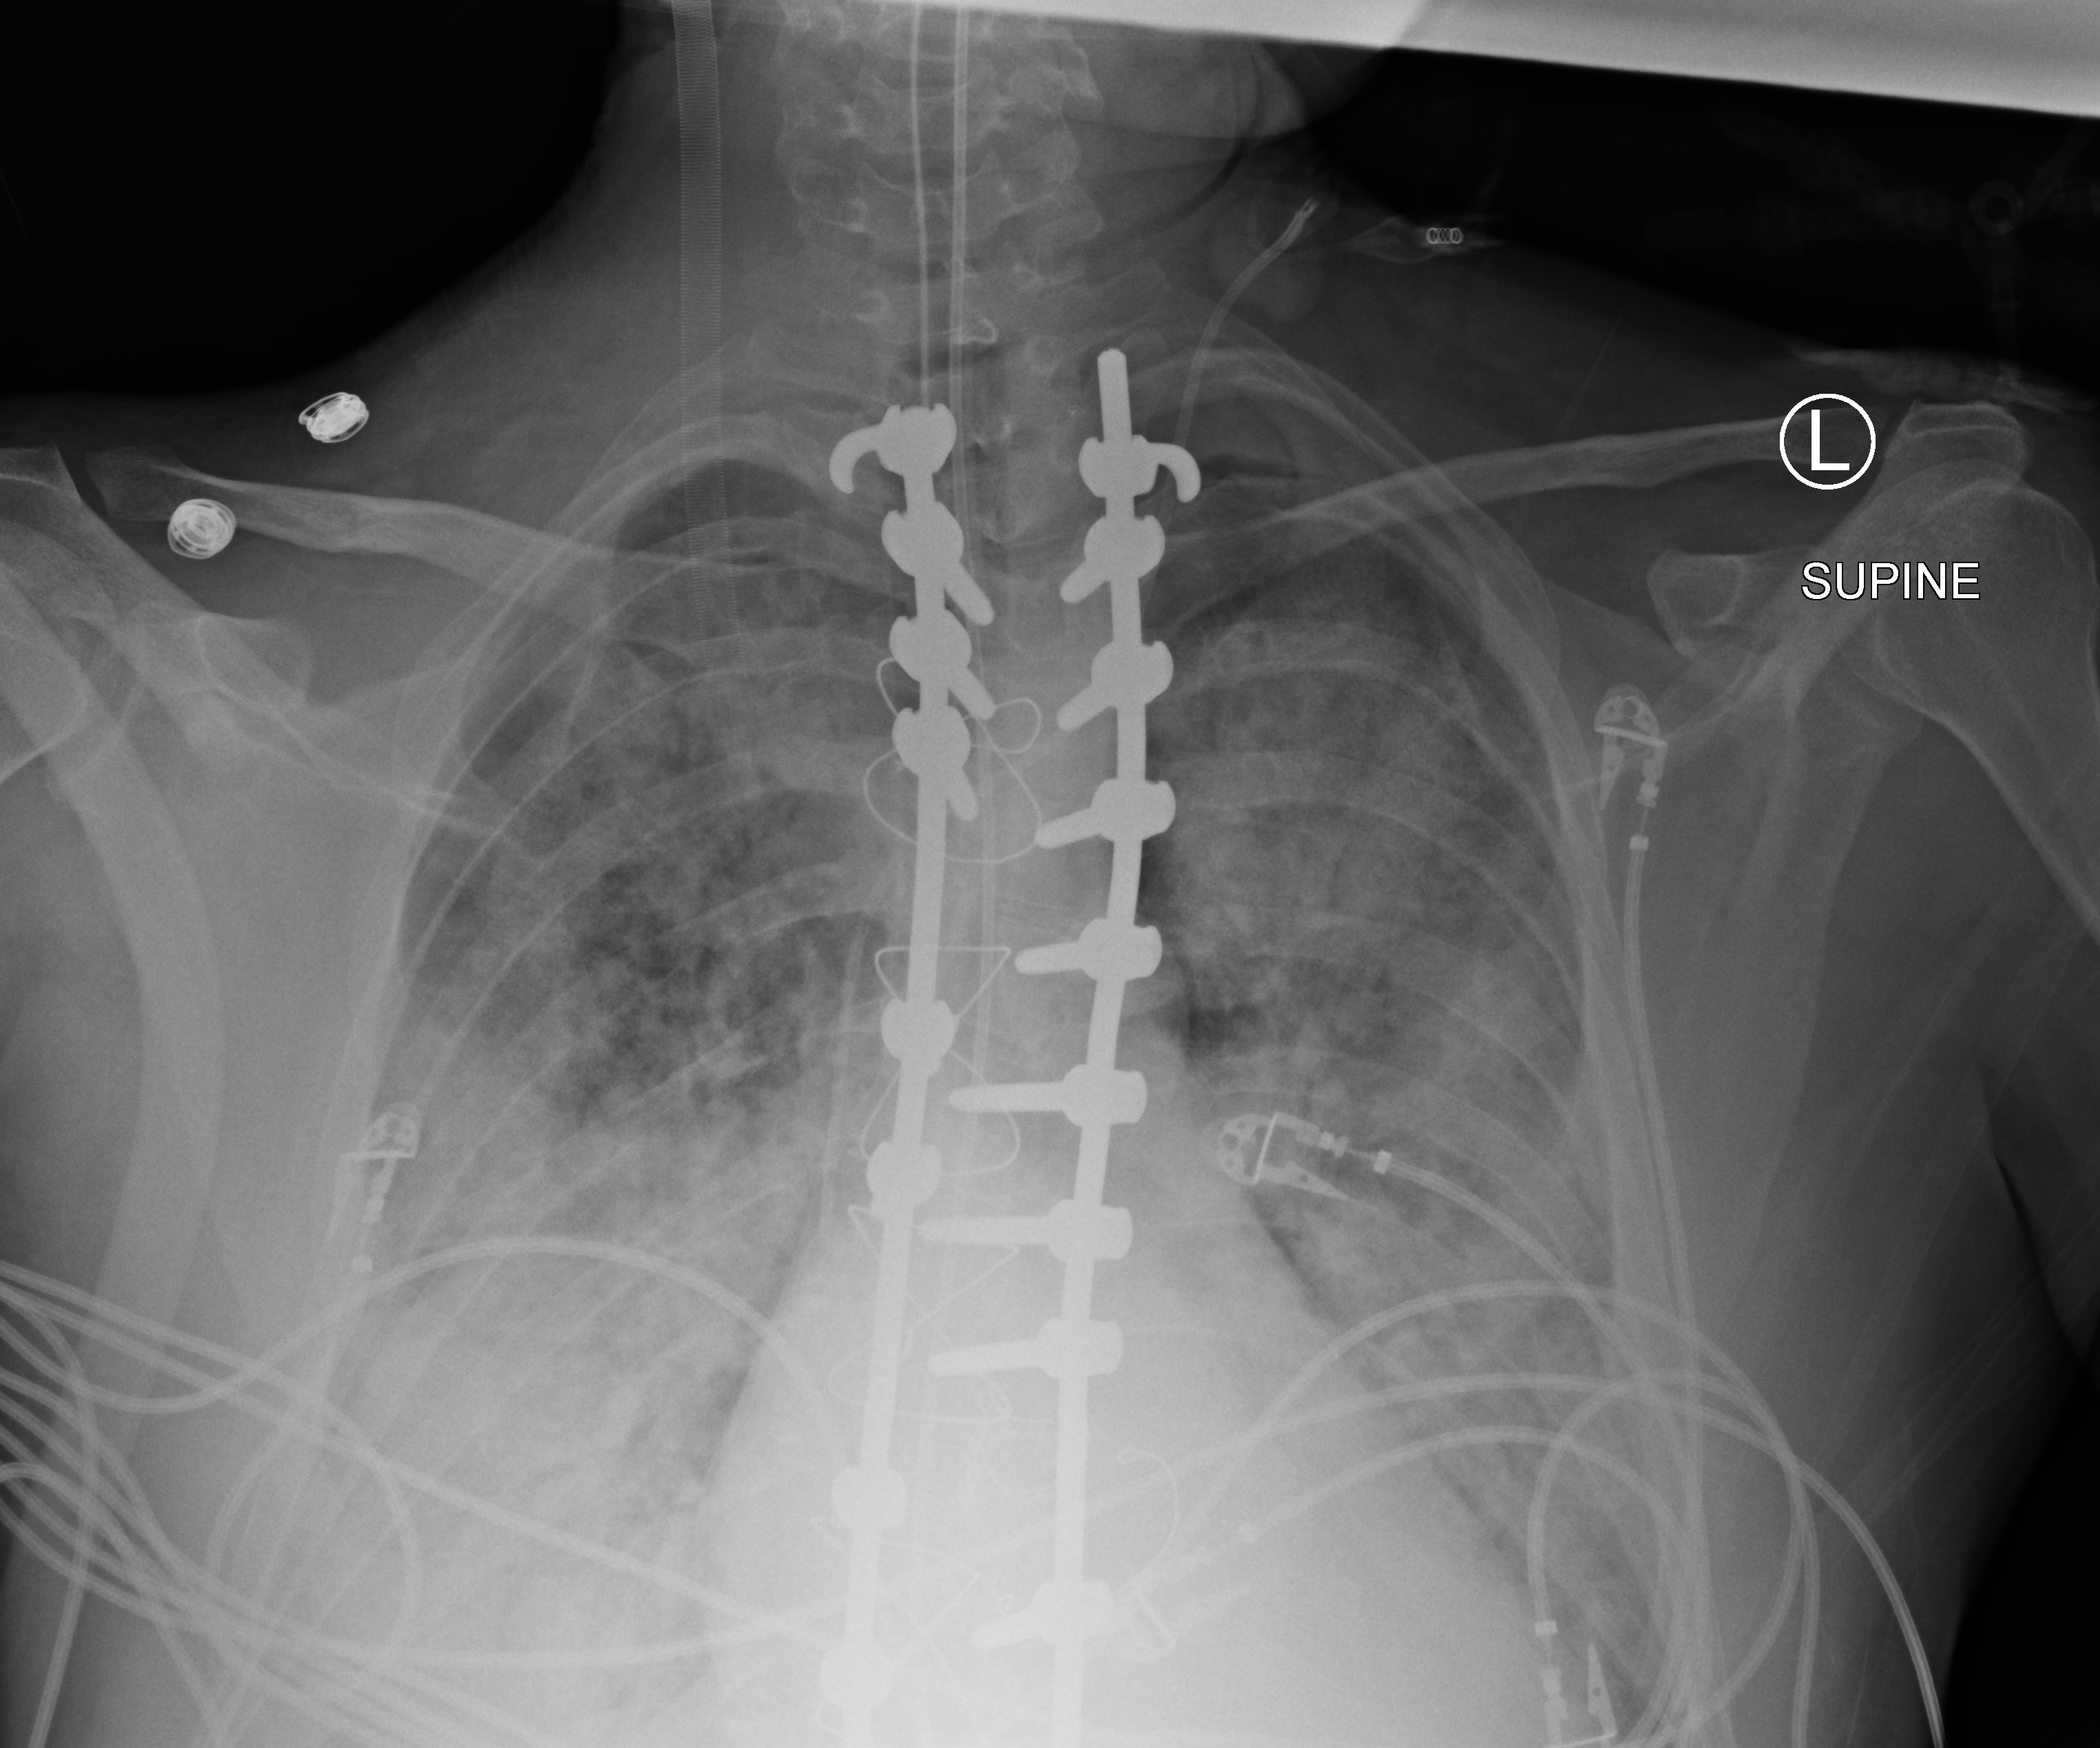
Chest X-ray (portable); anteroposterior (AP) projection. Patient hospitalised with COVID-19, aged 18–59 years.
From the hospital-stay record, not from the radiograph (when in the stay this image was taken is not recorded): mechanically ventilated during this hospital stay: yes.